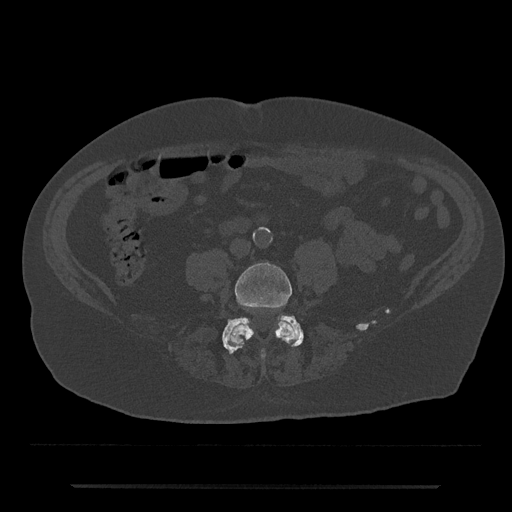
CT including the spine, one axial slice. Reconstruction kernel Br40s/3. 120 kVp. Bone window (W 1800 / L 400 HU). 0.5 mm slice thickness. 512 × 512 image matrix, field of view 434 × 434 mm. Male patient, age 80 years. Case-level facts recorded for this patient, not image findings: primary cancer: prostate.
Outlined on this slice (semi-automatically segmented with operator editing):
- L4 vertebra: bounding box (x1, y1, x2, y2) in pixels: (228, 263, 297, 358)
- L5 vertebra: (222, 315, 303, 354)